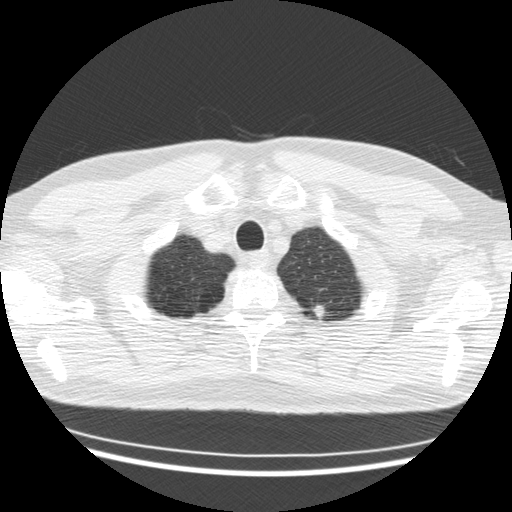
Low-dose screening chest CT, one axial slice. Position 157 of 176 along the scan axis. Lung window (W 1500 / L -600 HU). 512 × 512 image matrix.
Annotated regions visible in this slice (expert manual segmentation):
- lesion 1 (tumor, upper lobe of left lung): bounding box <313,305,325,319> (left, top, right, bottom; pixels)